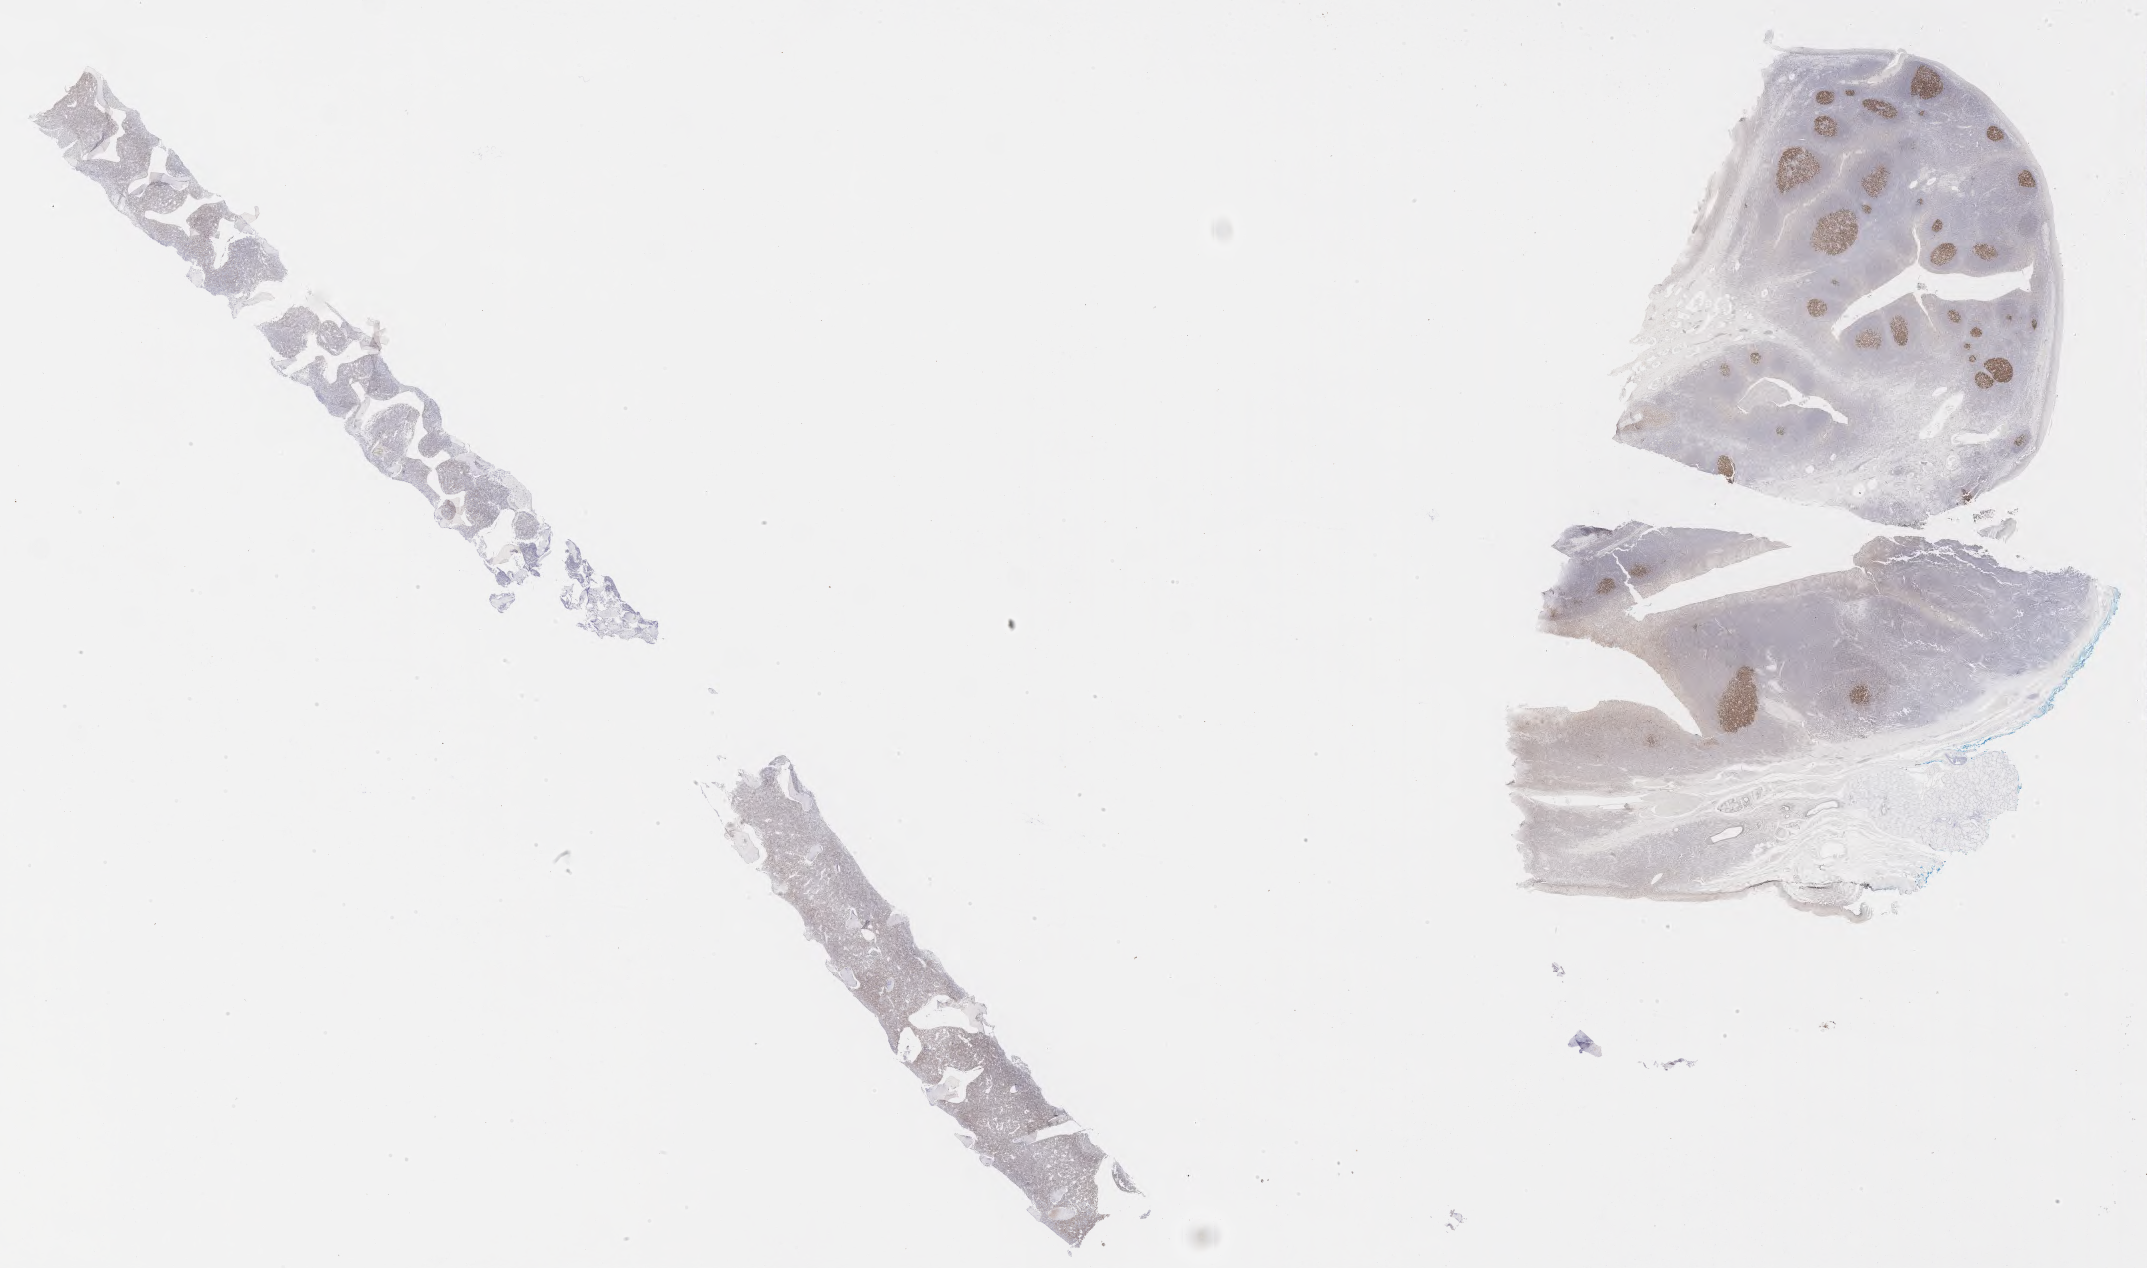
IHC for BCL6, whole-slide image, whole scanned area (about 34.7 x 20.5 mm) shown as a low-resolution overview. Specimen: tumor tissue. Male, age 7 years at initial diagnosis.
Diagnosis: Burkitt lymphoma, NOS.